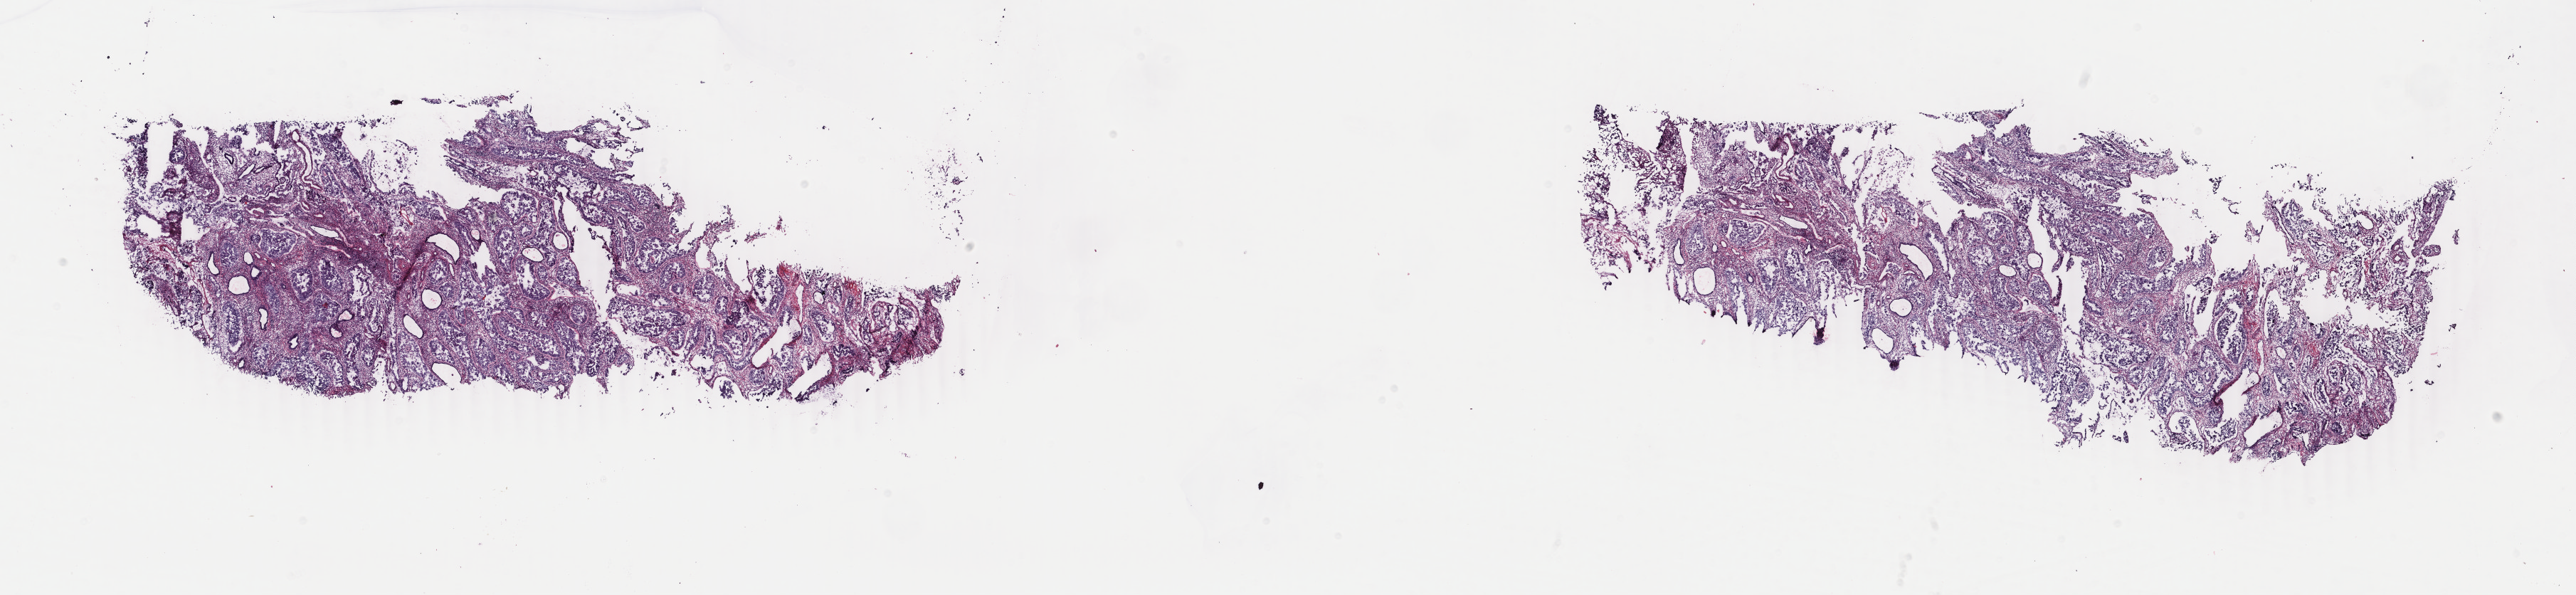
Hematoxylin and eosin (H&E) stained whole-slide image, whole scanned area (about 28.8 x 6.6 mm, from a 40x scan) shown as a low-resolution overview. Frozen section from the bottom of the tissue portion. Primary tumour sample from the uterus. Female patient; age at initial diagnosis 64 years. Histologic grade: G3 (poorly differentiated). Pathologist review of this section (percent, as recorded): tumour cells 75%, tumour nuclei 75%, normal cells 10%, stromal cells 5%, necrosis 10%. Inflammatory infiltration, as recorded: lymphocyte infiltration 30%, monocyte infiltration 15%, neutrophil infiltration 25%.
Histologic diagnosis: Serous cystadenocarcinoma, NOS (endometrium). Lymph nodes positive (case pathology): 0 of 3 examined. FIGO stage: IIIC1.